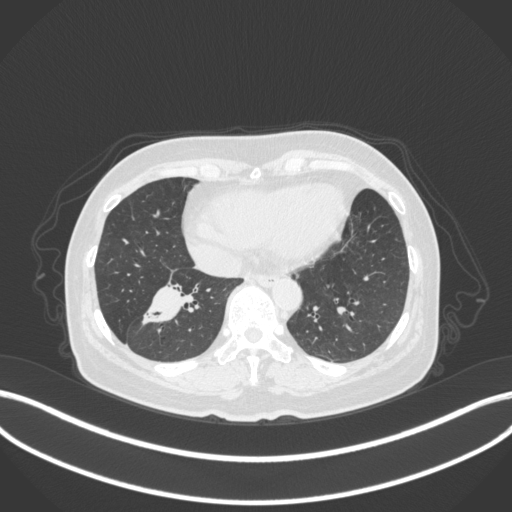
Chest CT, one axial slice. Slice 124 of 429 in the series (ordered by position). Reconstruction kernel B31f. 120 kVp. Lung window (W 1500 / L -600 HU). 512 × 512 image matrix. Female patient, age 67 years. Case-level facts recorded for this patient, not image findings: clinical TNM (as recorded): T1c N1 M0.
Structures marked on this image (rectangle marked by the reading radiologist):
- lung tumour (recorded histology: adenocarcinoma): bounding box (x1, y1, x2, y2) in pixels: (137, 279, 203, 330)